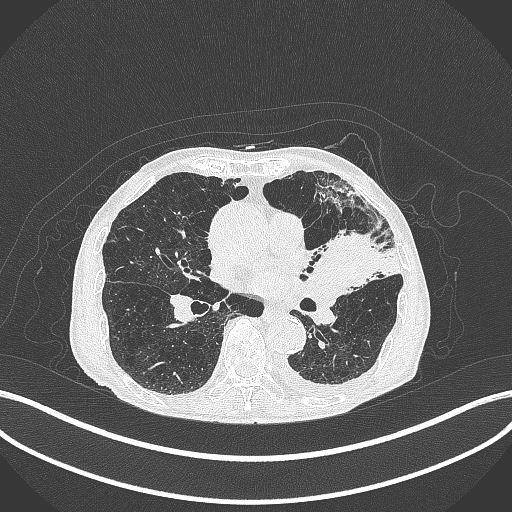
Chest CT, one axial slice. Position 191 of 385 along the scan axis. Reconstruction kernel B70f. 120 kVp. Lung window (W 1500 / L -600 HU). 1 mm slice thickness. 512 × 512 image matrix, field of view 400 × 400 mm. Patient: male, 90 years or older. From the clinical record (not read from this slice): clinical TNM (as recorded): T2b N1 M0.
Annotated regions visible in this slice (rectangle marked by the reading radiologist):
- lung tumour (recorded histology: squamous cell carcinoma): bounding box <305,221,384,294> (left, top, right, bottom; pixels)